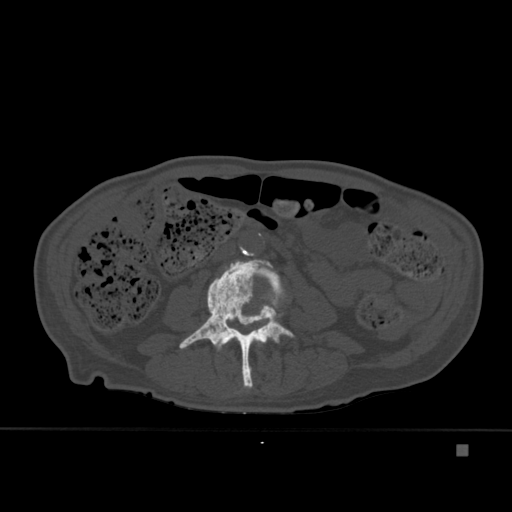
CT including the spine, one axial slice. Position 142 of 451 along the scan axis. Bone window (W 1800 / L 400 HU). 512 × 512 image matrix, field of view 378 × 378 mm. Patient: male, 75 years. From the clinical record (not read from this slice): primary cancer: prostate.
Structures marked on this image (semi-automatically segmented with operator editing):
- L3 vertebra: bounding box [x1, y1, x2, y2] px = [179, 259, 295, 389]